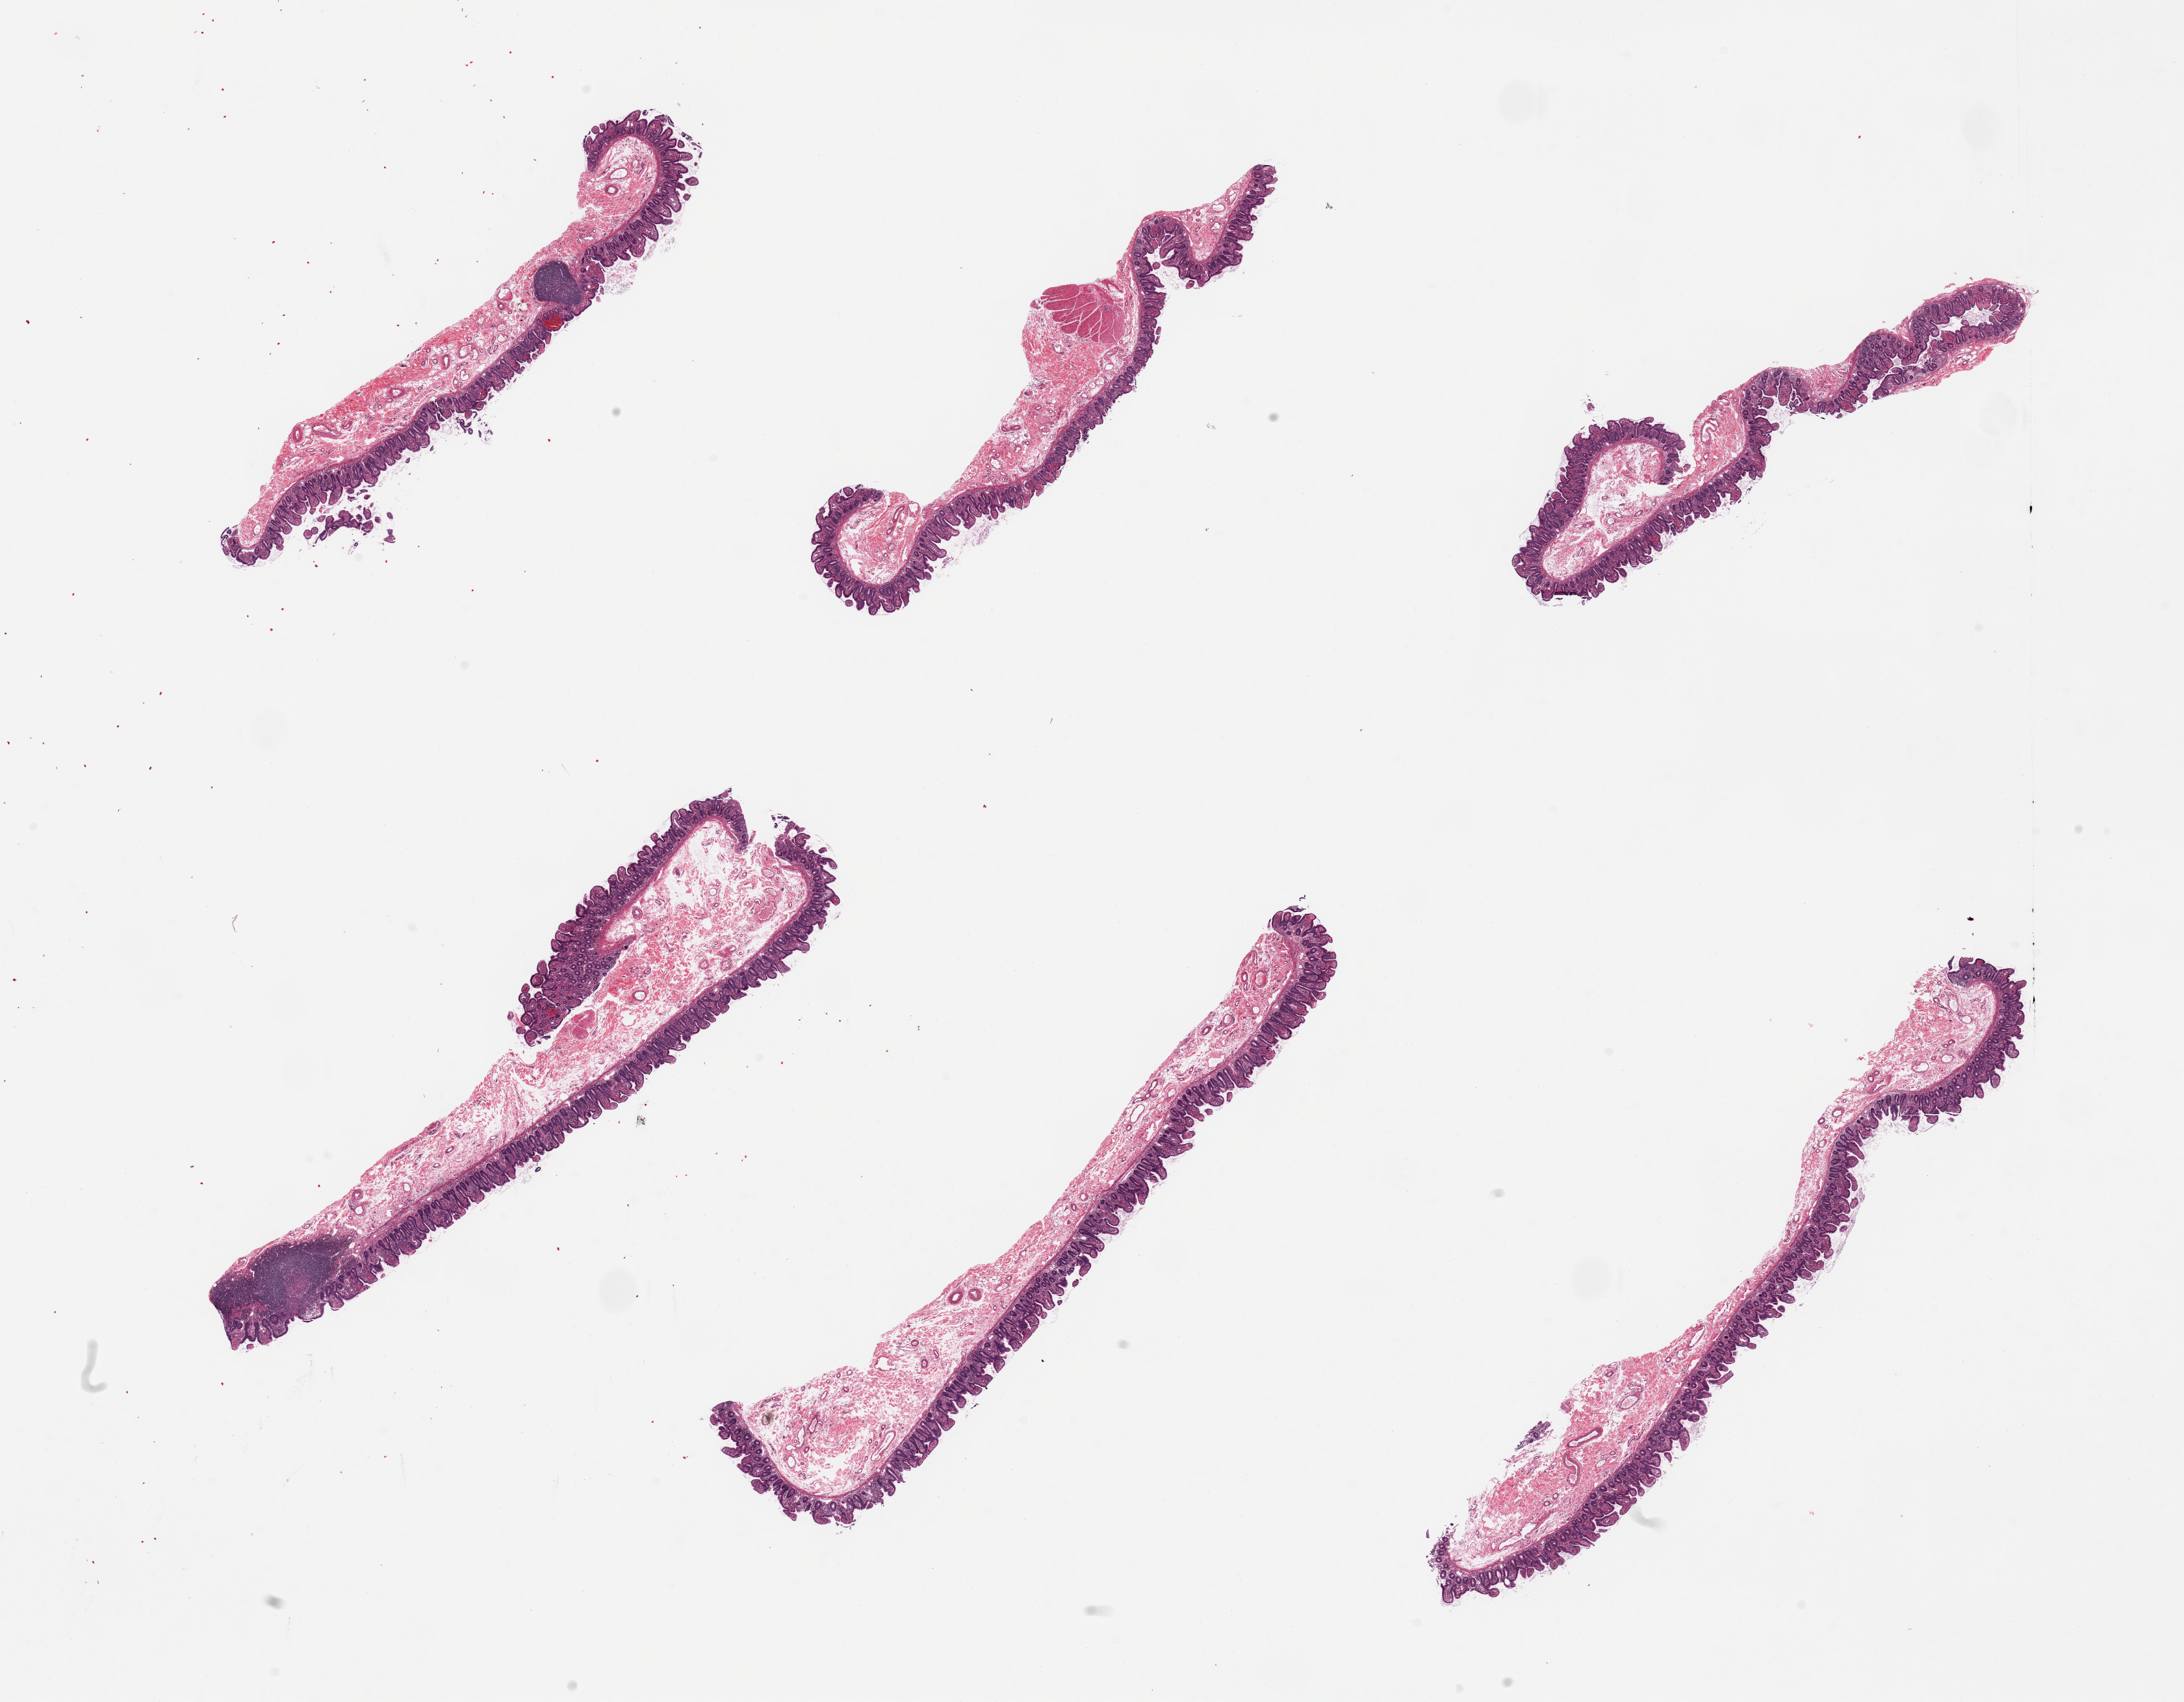
Whole-slide image, hematoxylin and eosin (H&E) stain, whole scanned area (about 26.6 x 20.7 mm, acquisition: 20x scan) shown as a low-resolution overview. PAXgene-fixed paraffin-embedded (PFPE) section. Section of ileum (target tissue). Donor tissue sample. Male donor.
- pathologist's review note for this sample: 6 pieces, minimal lymphoid tissue